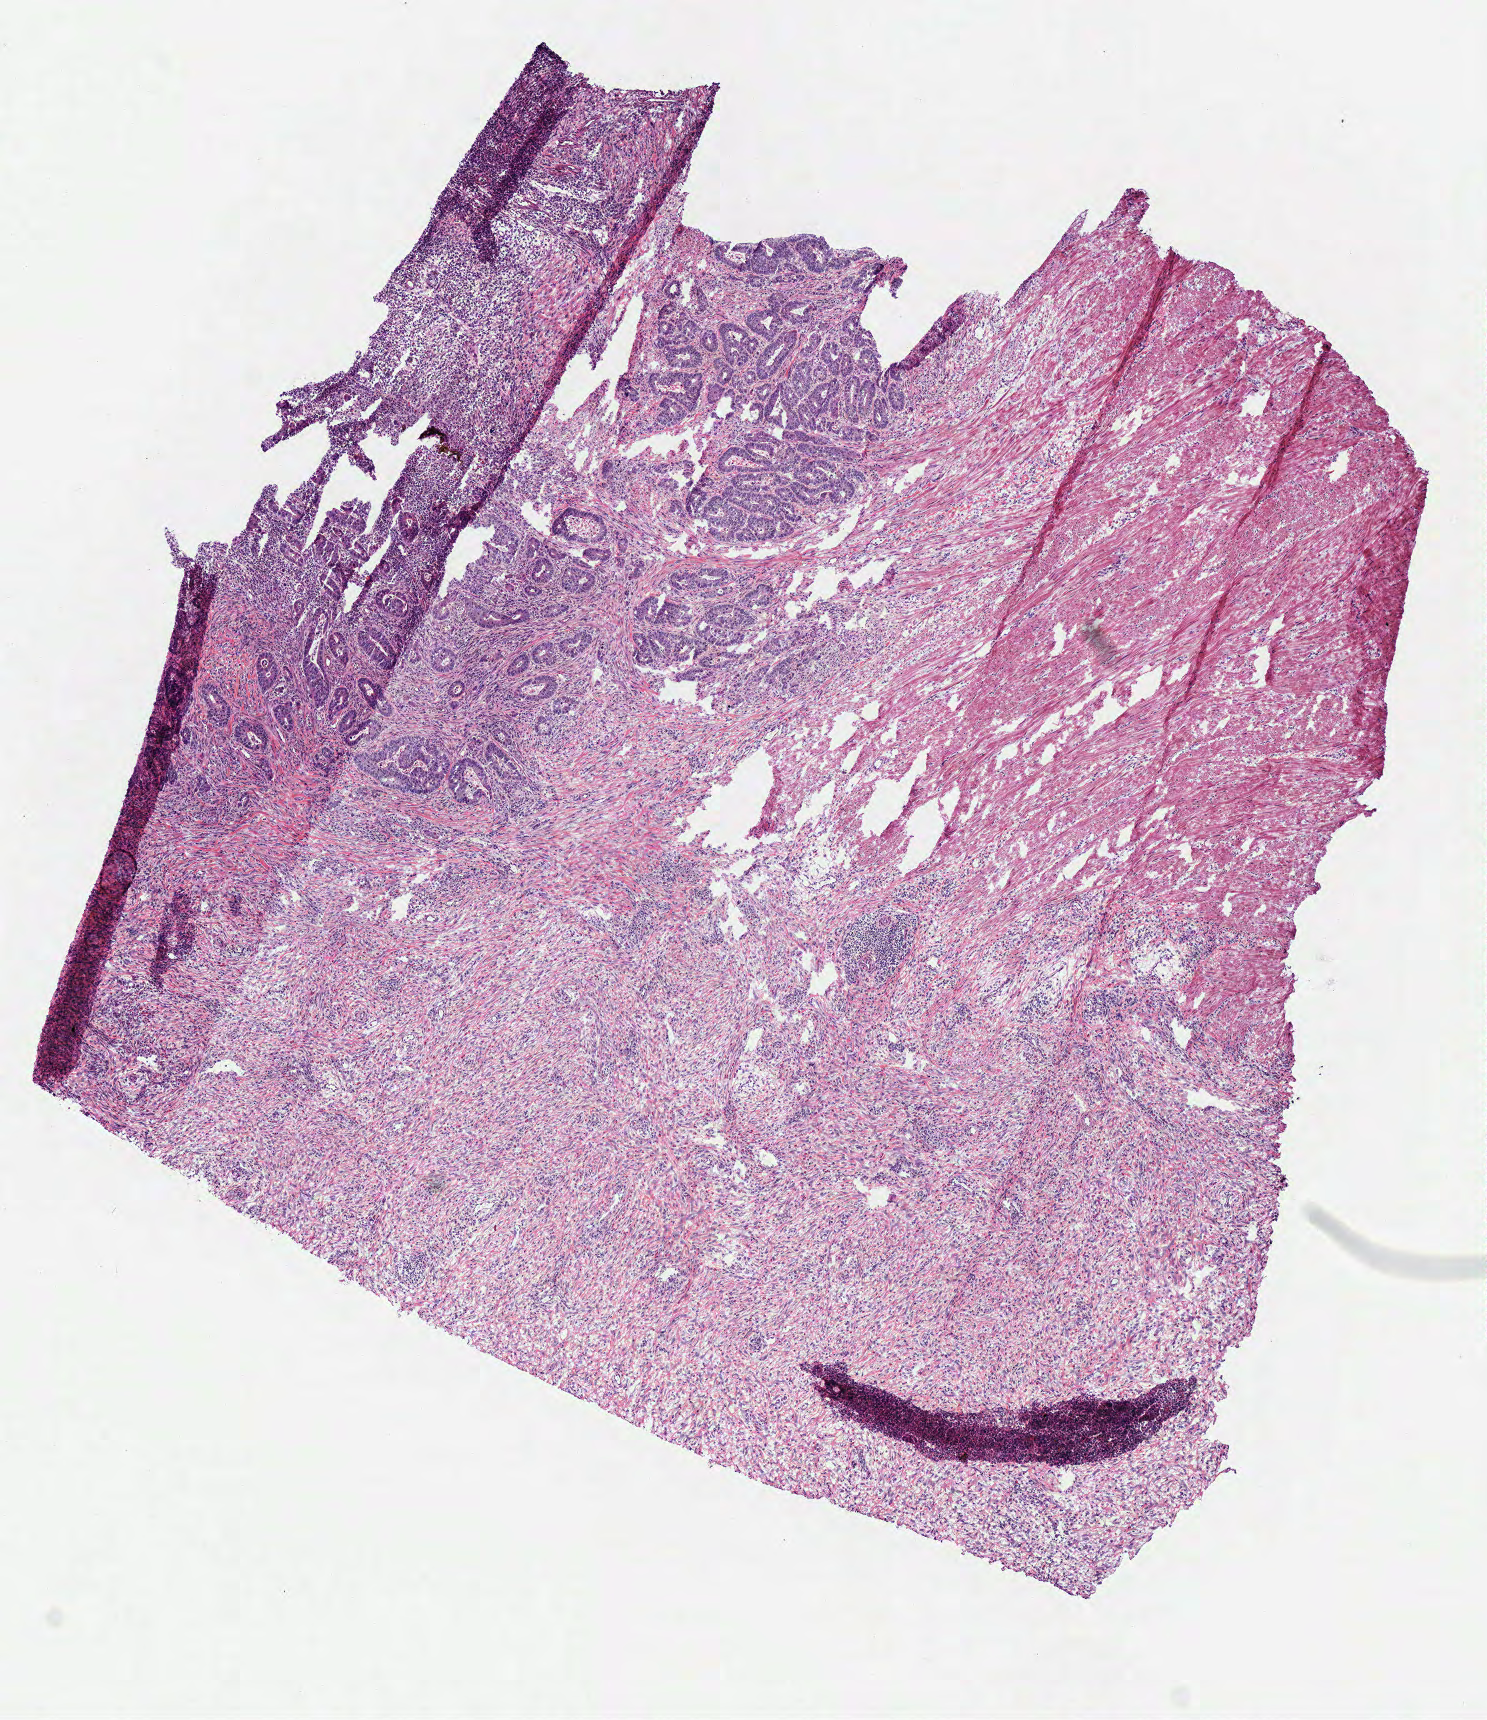
Whole-slide histology image, H&E-stained, whole scanned area (about 5.9 x 6.8 mm) shown as a low-resolution overview; frozen section; primary tumour sample from the colon. Patient: male, age at initial diagnosis 65 years. Composition of this section per pathologist review: tumour cells 10%, tumour nuclei 10%.
Pathologic diagnosis: Adenocarcinoma, NOS (sigmoid colon).